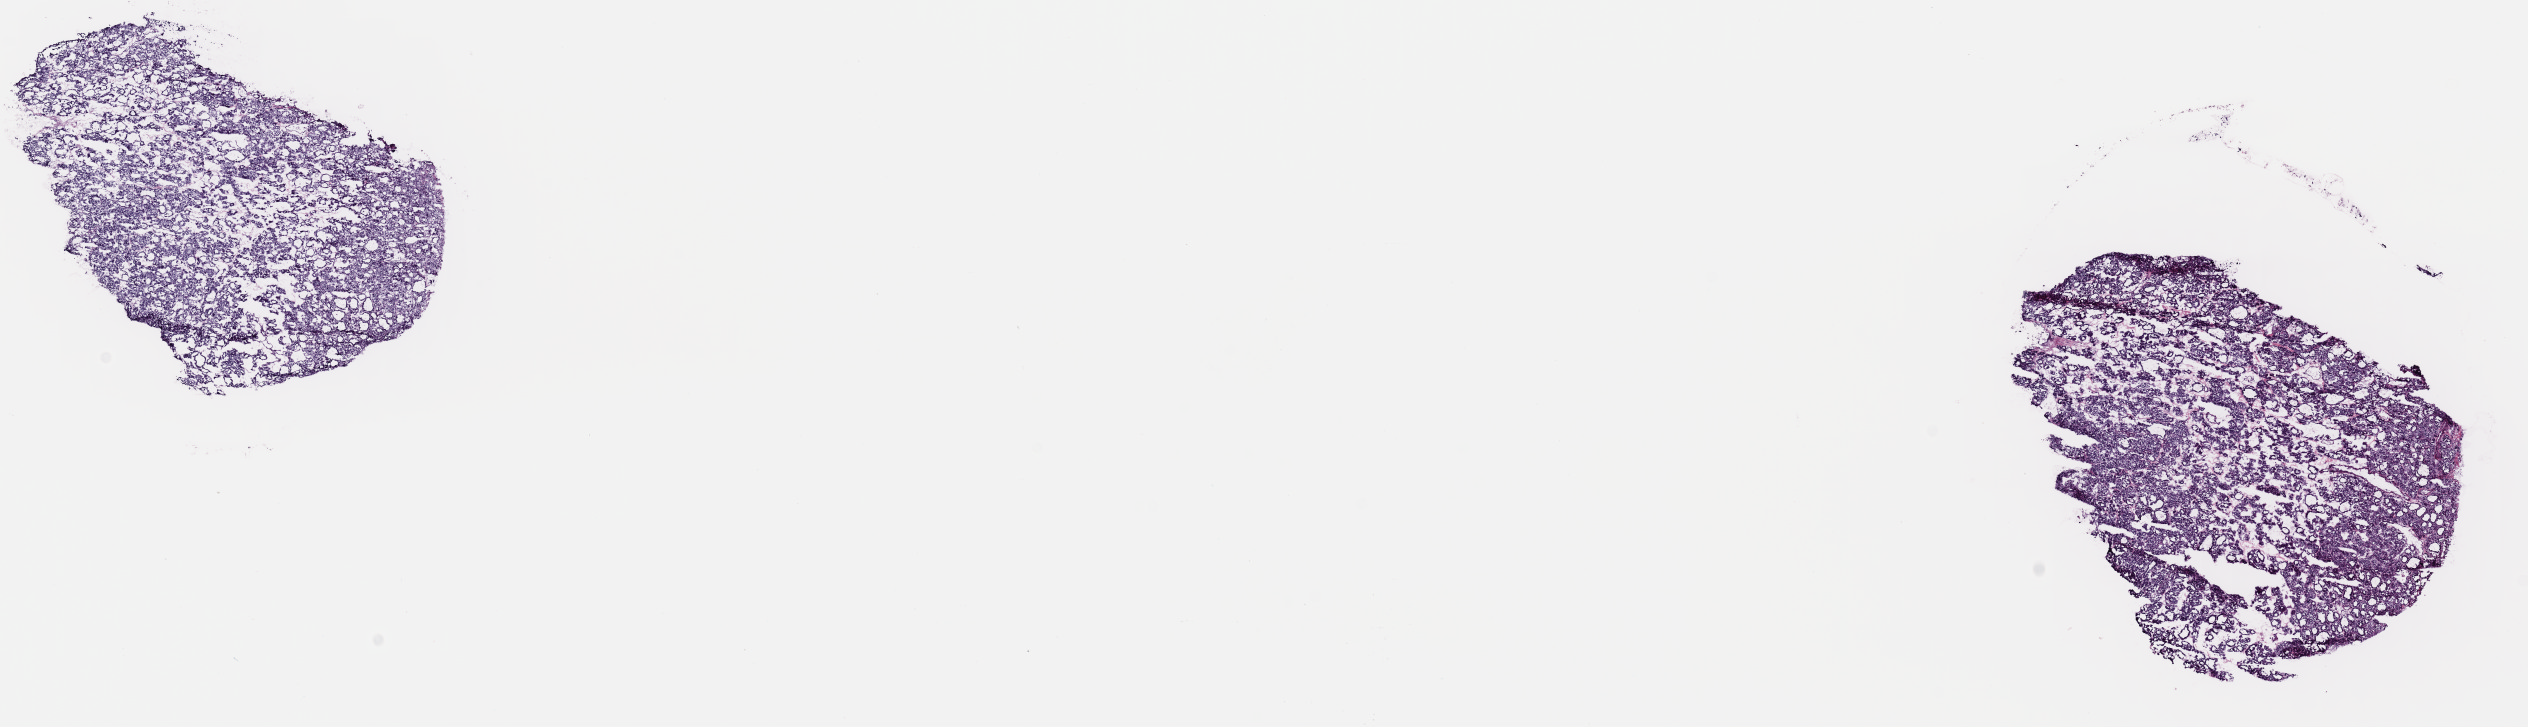
H&E whole-slide image, whole scanned area (about 20.0 x 5.7 mm, from a 40x scan) shown as a low-resolution overview. Frozen section from the top of the tissue portion. Thyroid, primary tumour sample. Female patient; age at initial diagnosis 20 years. Slide review estimates, as recorded: tumour cells 98%, tumour nuclei 100%, normal cells 0%, stromal cells 2%, necrosis 0%. Inflammatory infiltration, as recorded: lymphocyte infiltration 0%, monocyte infiltration 0%, neutrophil infiltration 0%.
TNM: T1b N0 MX. Diagnosis: Papillary carcinoma, follicular variant (thyroid gland). AJCC pathologic stage: I (7th edition).